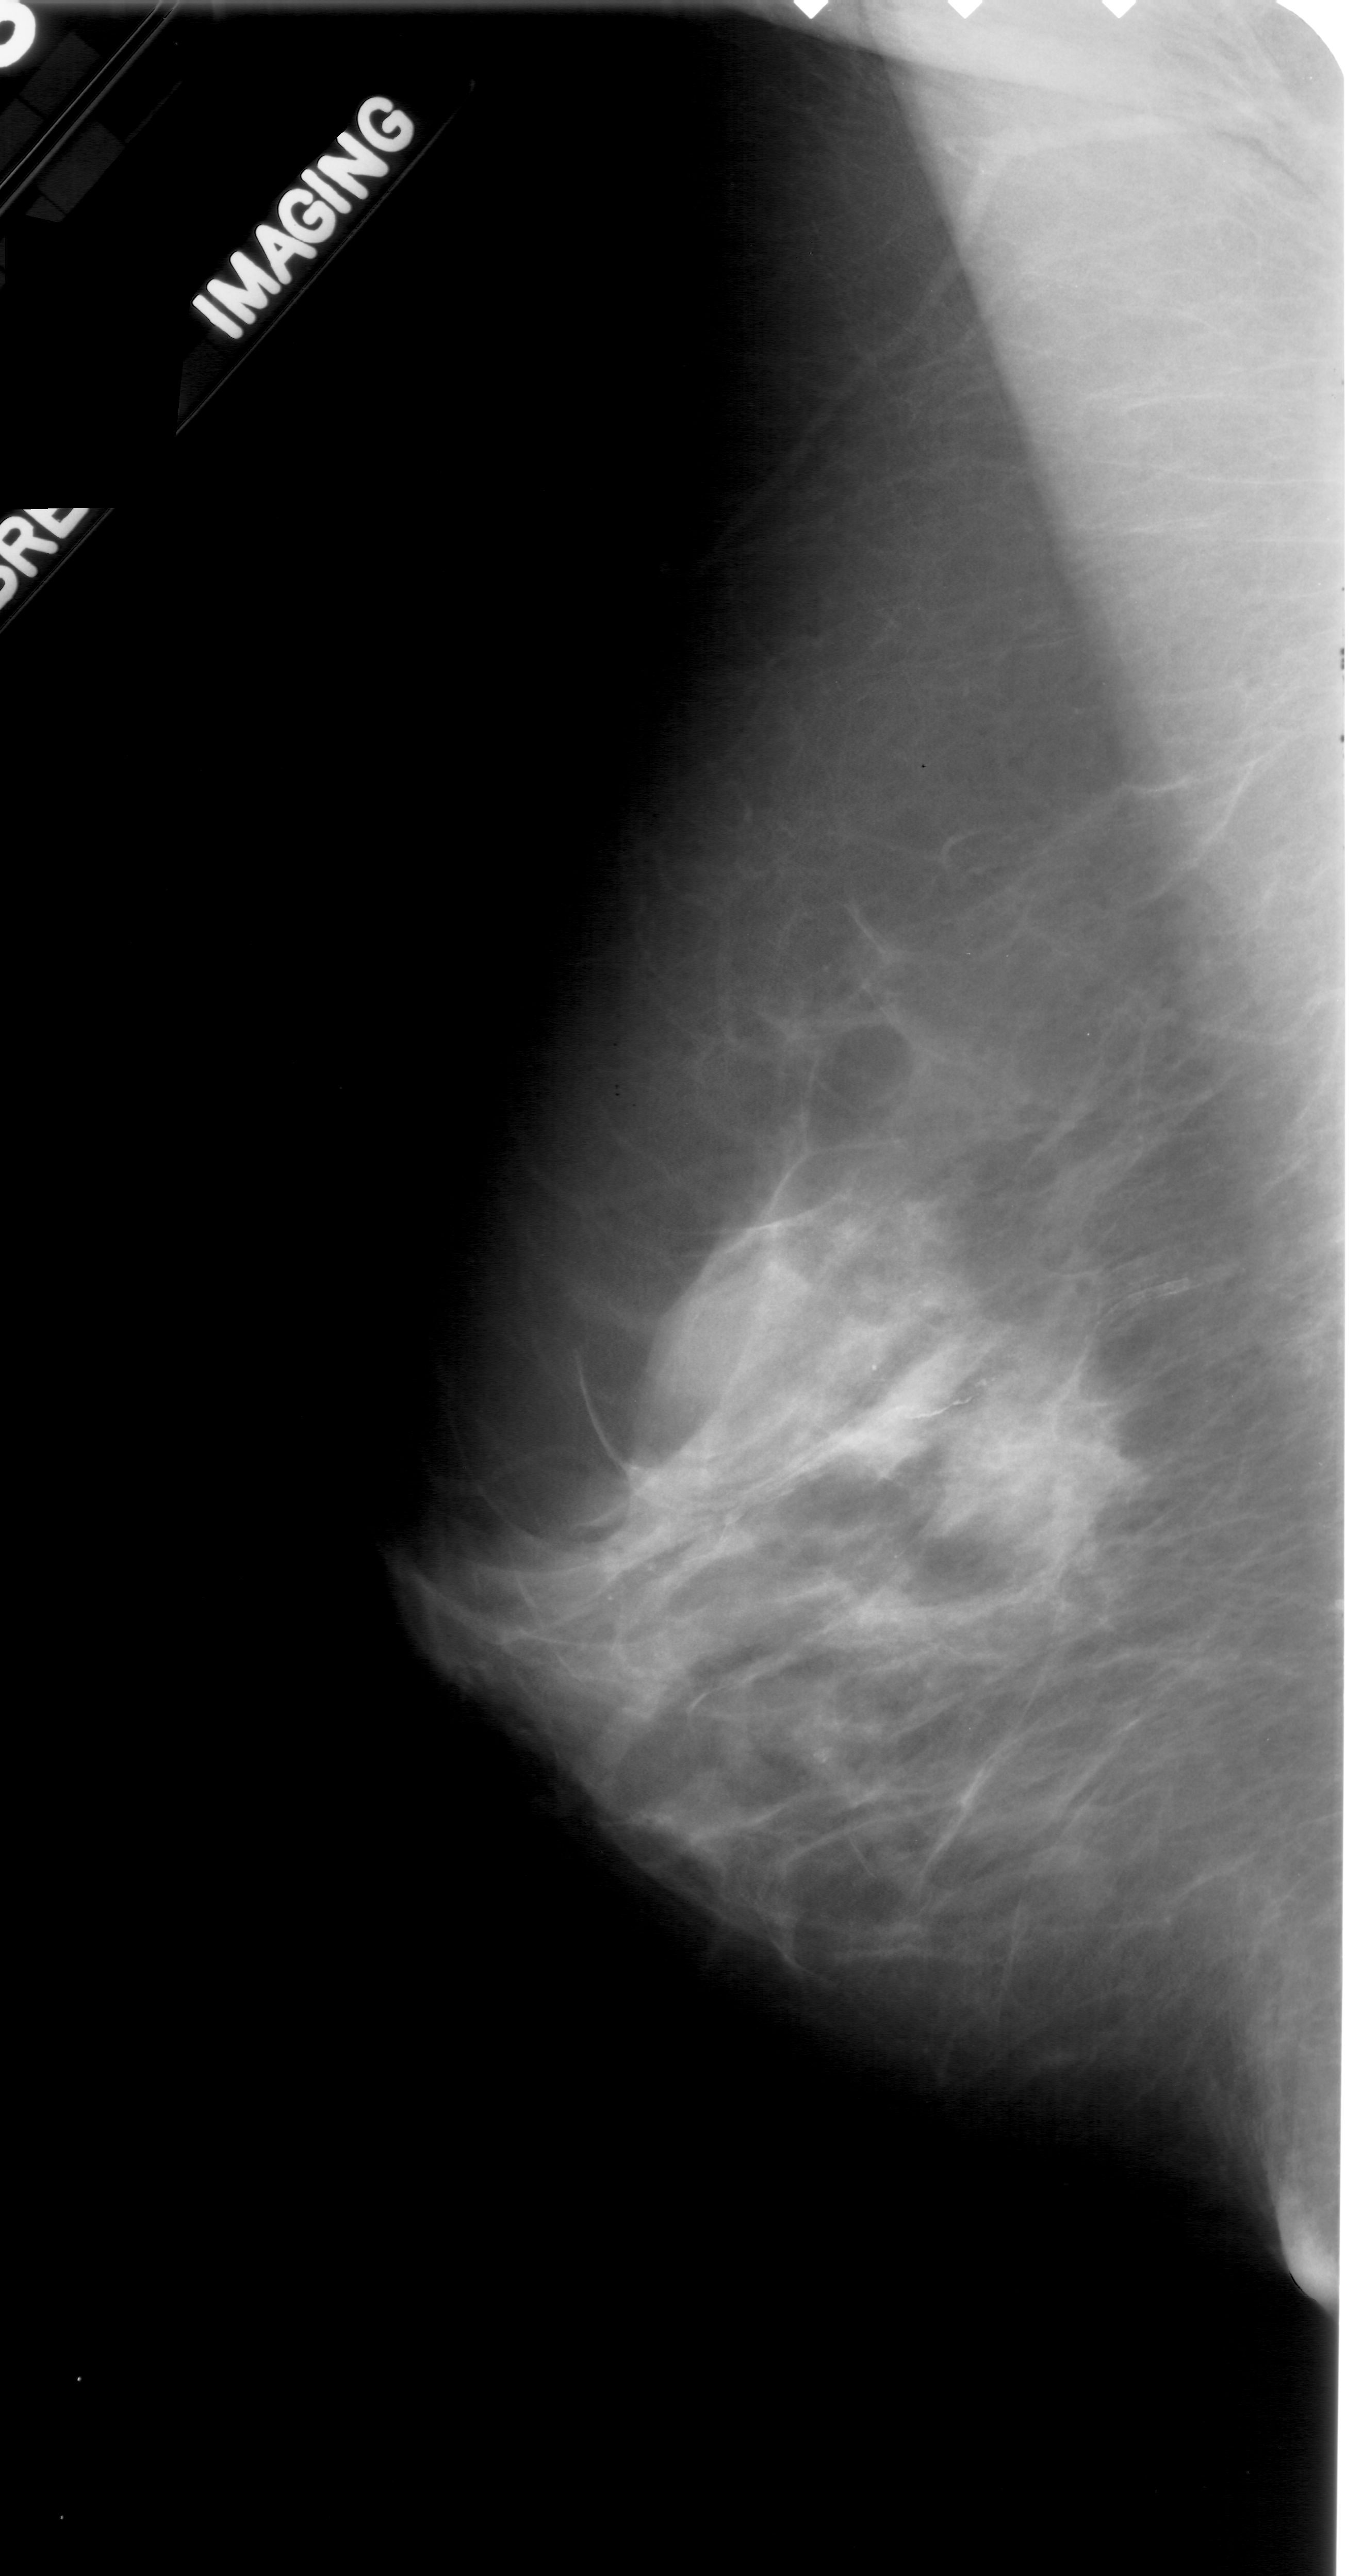
Mammogram (digitized film); left breast; MLO view; 1362 × 2576 image matrix.
Expert-marked regions of interest on this film, with their recorded descriptors:
- mass, shape oval, margins ill defined; BI-RADS assessment category 4; subtlety rating 4 on a 1 (subtle) to 5 (obvious) scale; pathology (as recorded): malignant: bounding box (x1, y1, x2, y2) in pixels: (648, 1279, 801, 1421)